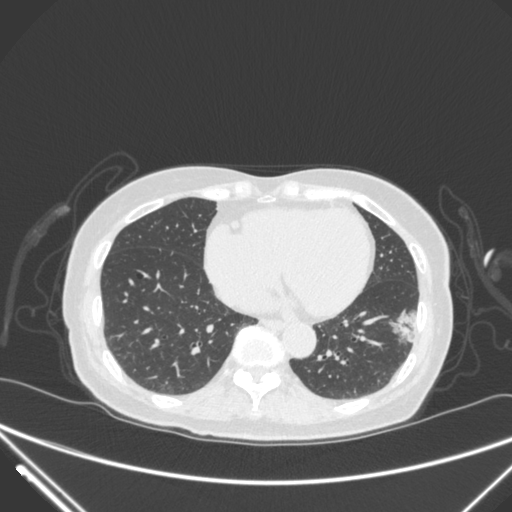
Chest CT, one axial slice. Slice 107 of 310 in the series (ordered by position). 120 kVp. Lung window (W 1500 / L -600 HU). 1 mm slice thickness. 512 × 512 image matrix. Patient: female, 82 years. Case-level facts recorded for this patient, not image findings: clinical TNM (as recorded): T1c N0 M0; histopathological grade: G2.
Outlined on this slice (bounding box drawn by a radiologist):
- lung tumour (recorded histology: adenocarcinoma): bounding box (x1, y1, x2, y2) in pixels: (381, 300, 423, 360)